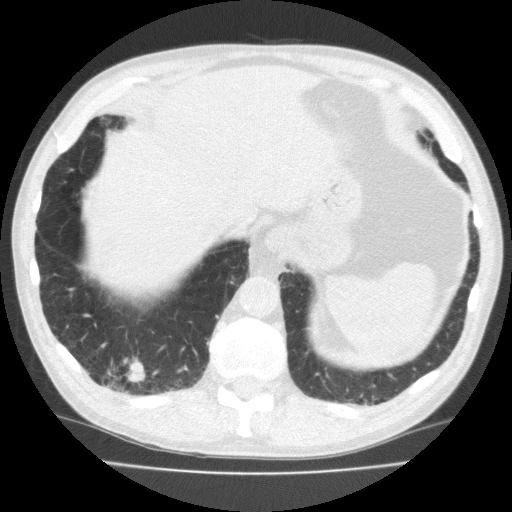
Axial slice from a low-dose chest CT screening exam. Second annual screen. Lung window (W 1500 / L -600 HU). Standard (soft-tissue) reconstruction kernel (FC10). 512 × 512 image matrix. Male, age 70 years at enrolment. Current smoker at enrolment.
- Expert-annotated lung lesion, bounding box [x1, y1, x2, y2] px = [89, 348, 159, 399].
- Screening reader's record for this exam (one nodule recorded; not confirmed to be the boxed lesion): non-calcified nodule or mass ≥4 mm, right lower lobe, 18 × 13 mm, spiculated (stellate) margins, soft tissue attenuation, pre-existing on the prior screen: no.
- Participant outcome: lung cancer diagnosed 64 days after this screen — squamous cell carcinoma, NOS, right lower lobe, moderately differentiated (G2), stage IA (AJCC 6th edition), 20 mm at pathology.